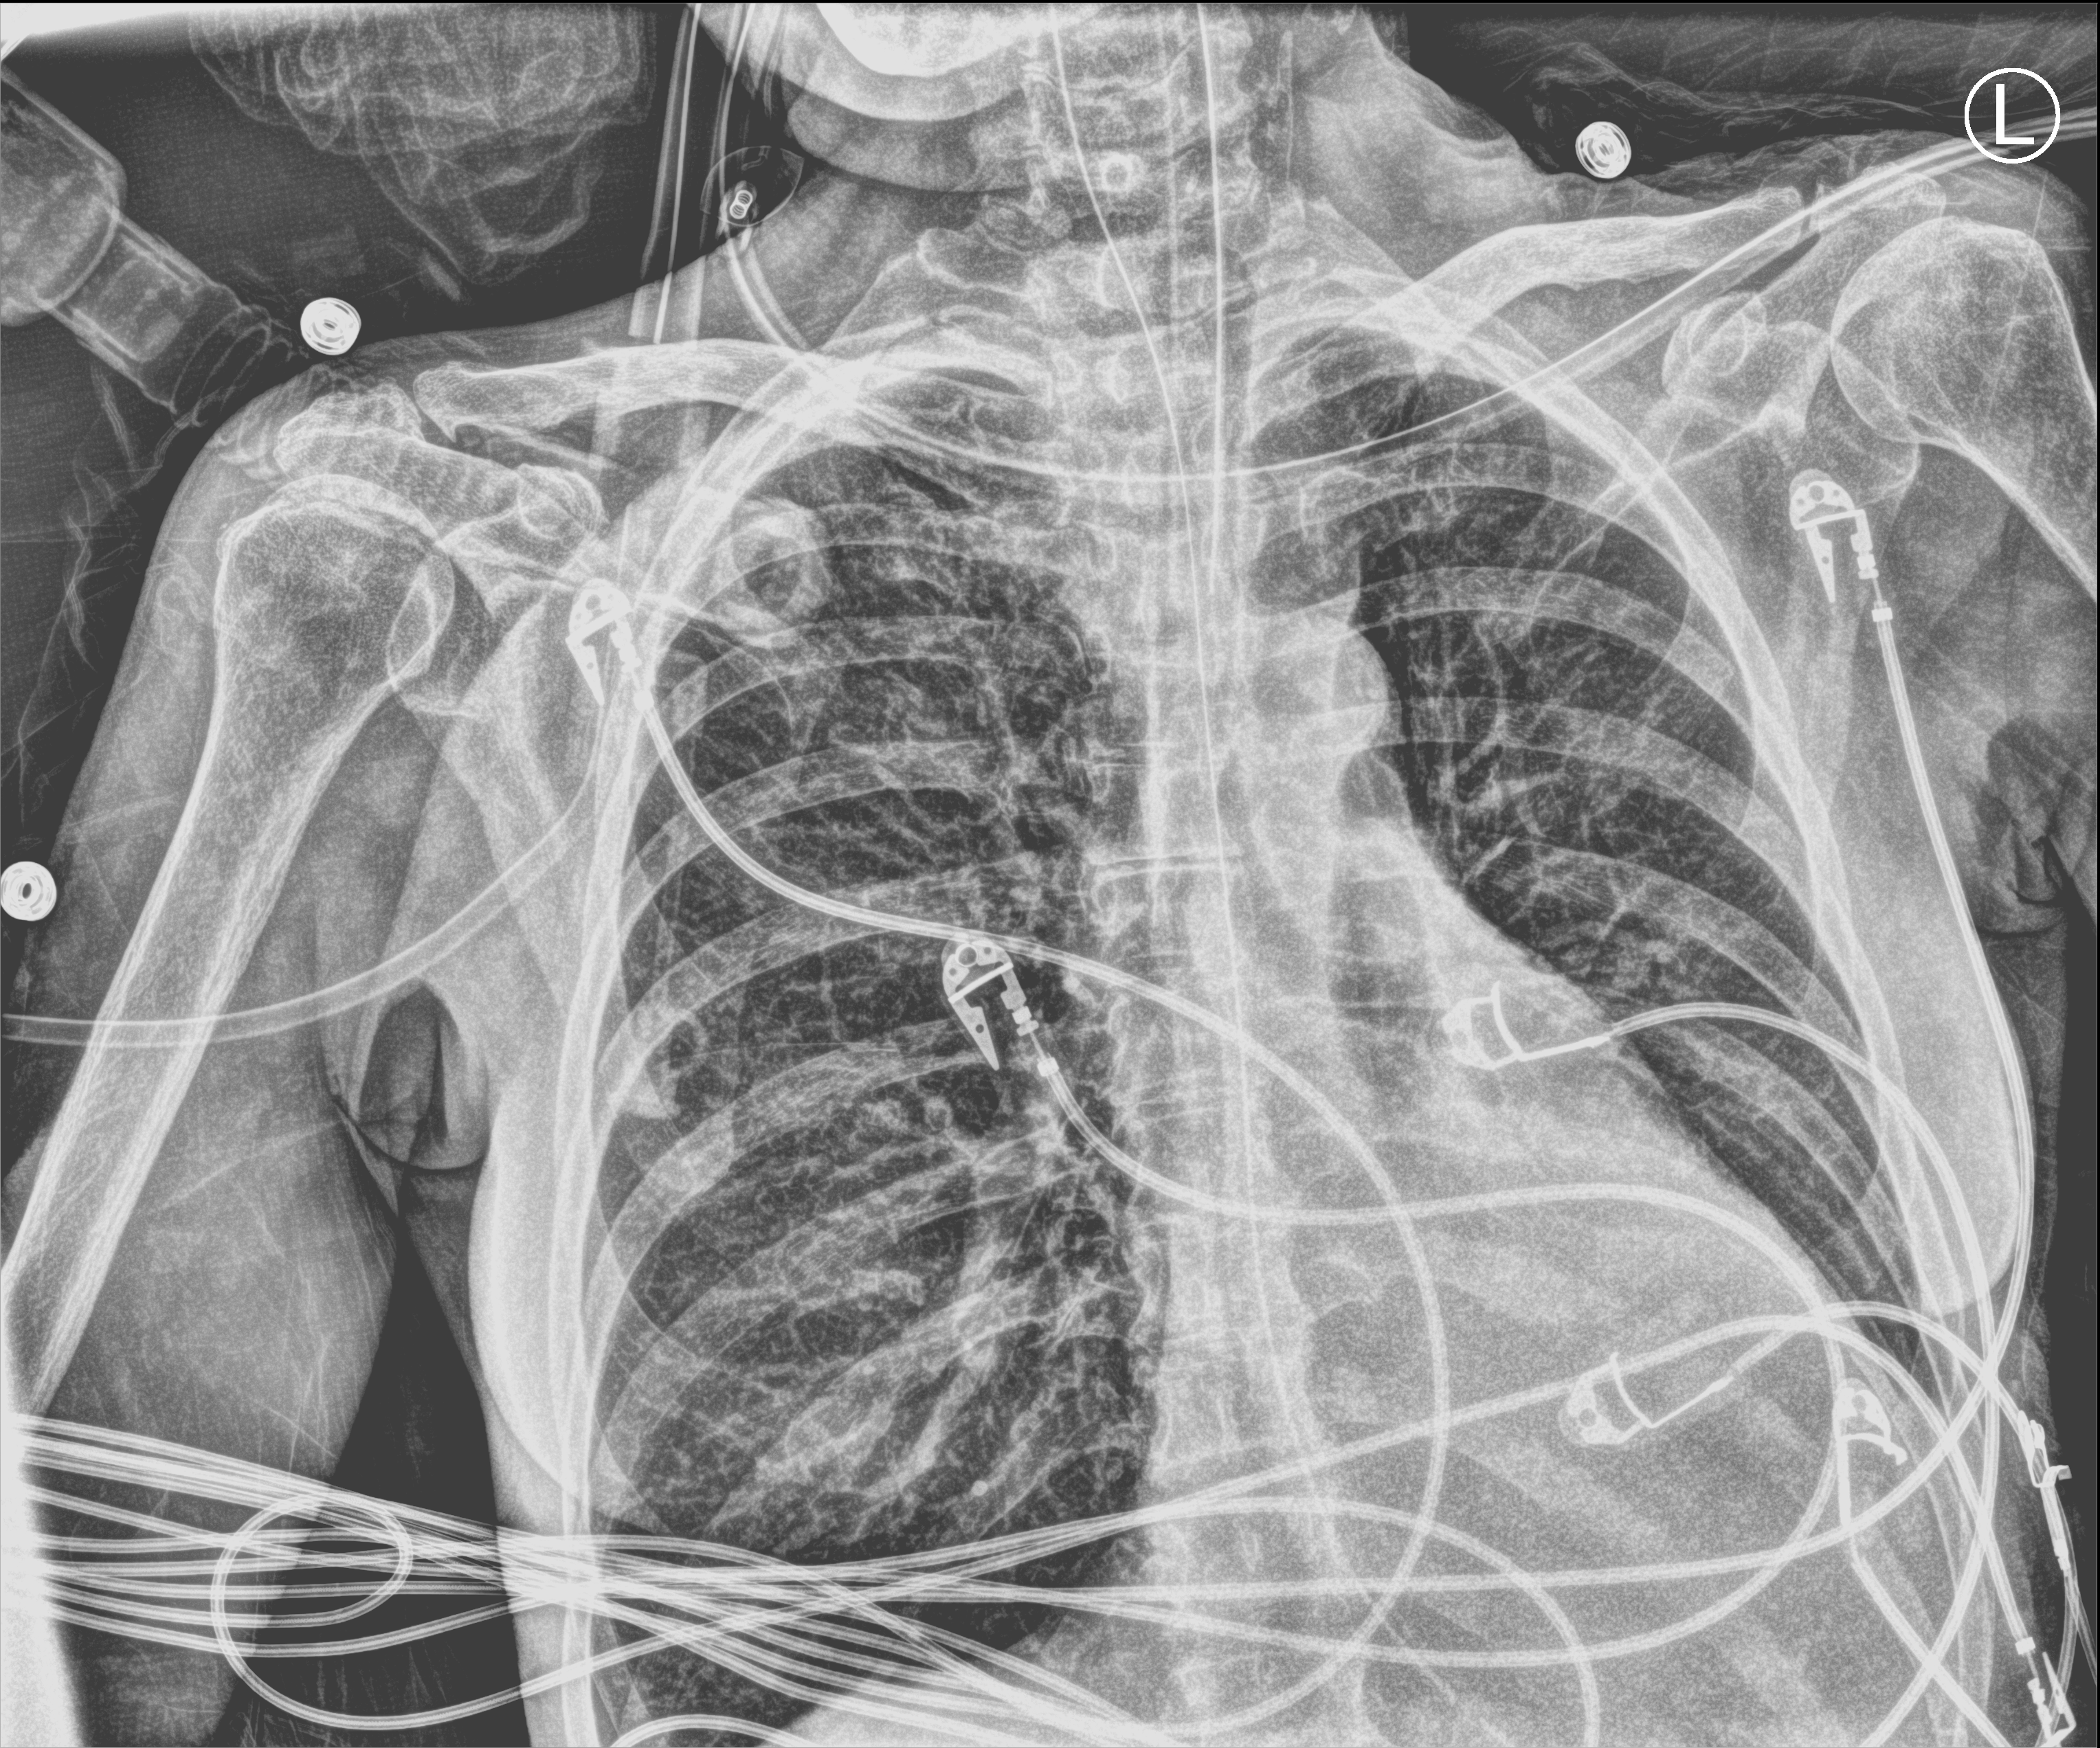
Bedside chest radiograph (computed radiography); anteroposterior (AP) projection. Female patient hospitalised with COVID-19, age 60–74 years.
Admission-level facts for this patient (not findings on this image; timing relative to this image not recorded): mechanically ventilated during this hospital stay: yes; length of hospital stay: 38 days; admitted to intensive care during this hospital stay: yes.